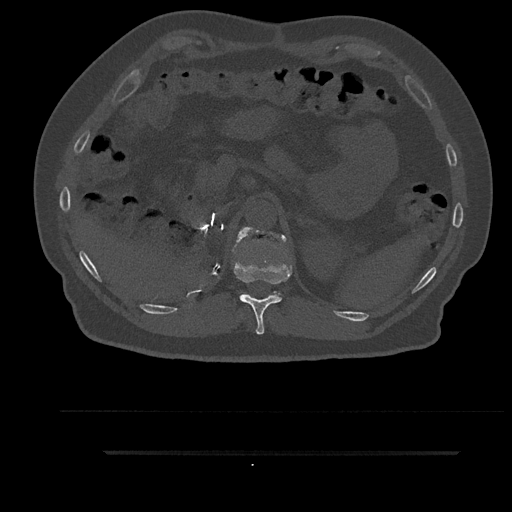
CT including the spine, one axial slice; bone window (W 1800 / L 400 HU); 512 × 512 image matrix, field of view 432 × 432 mm. Patient: male, 63 years. Case-level facts recorded for this patient, not image findings: primary cancer: renal.
Annotated regions visible in this slice (semi-automatically segmented with operator editing):
- T11 vertebra: bounding box [x1, y1, x2, y2] px = [234, 228, 292, 335]
- T12 vertebra: [233, 226, 286, 294]